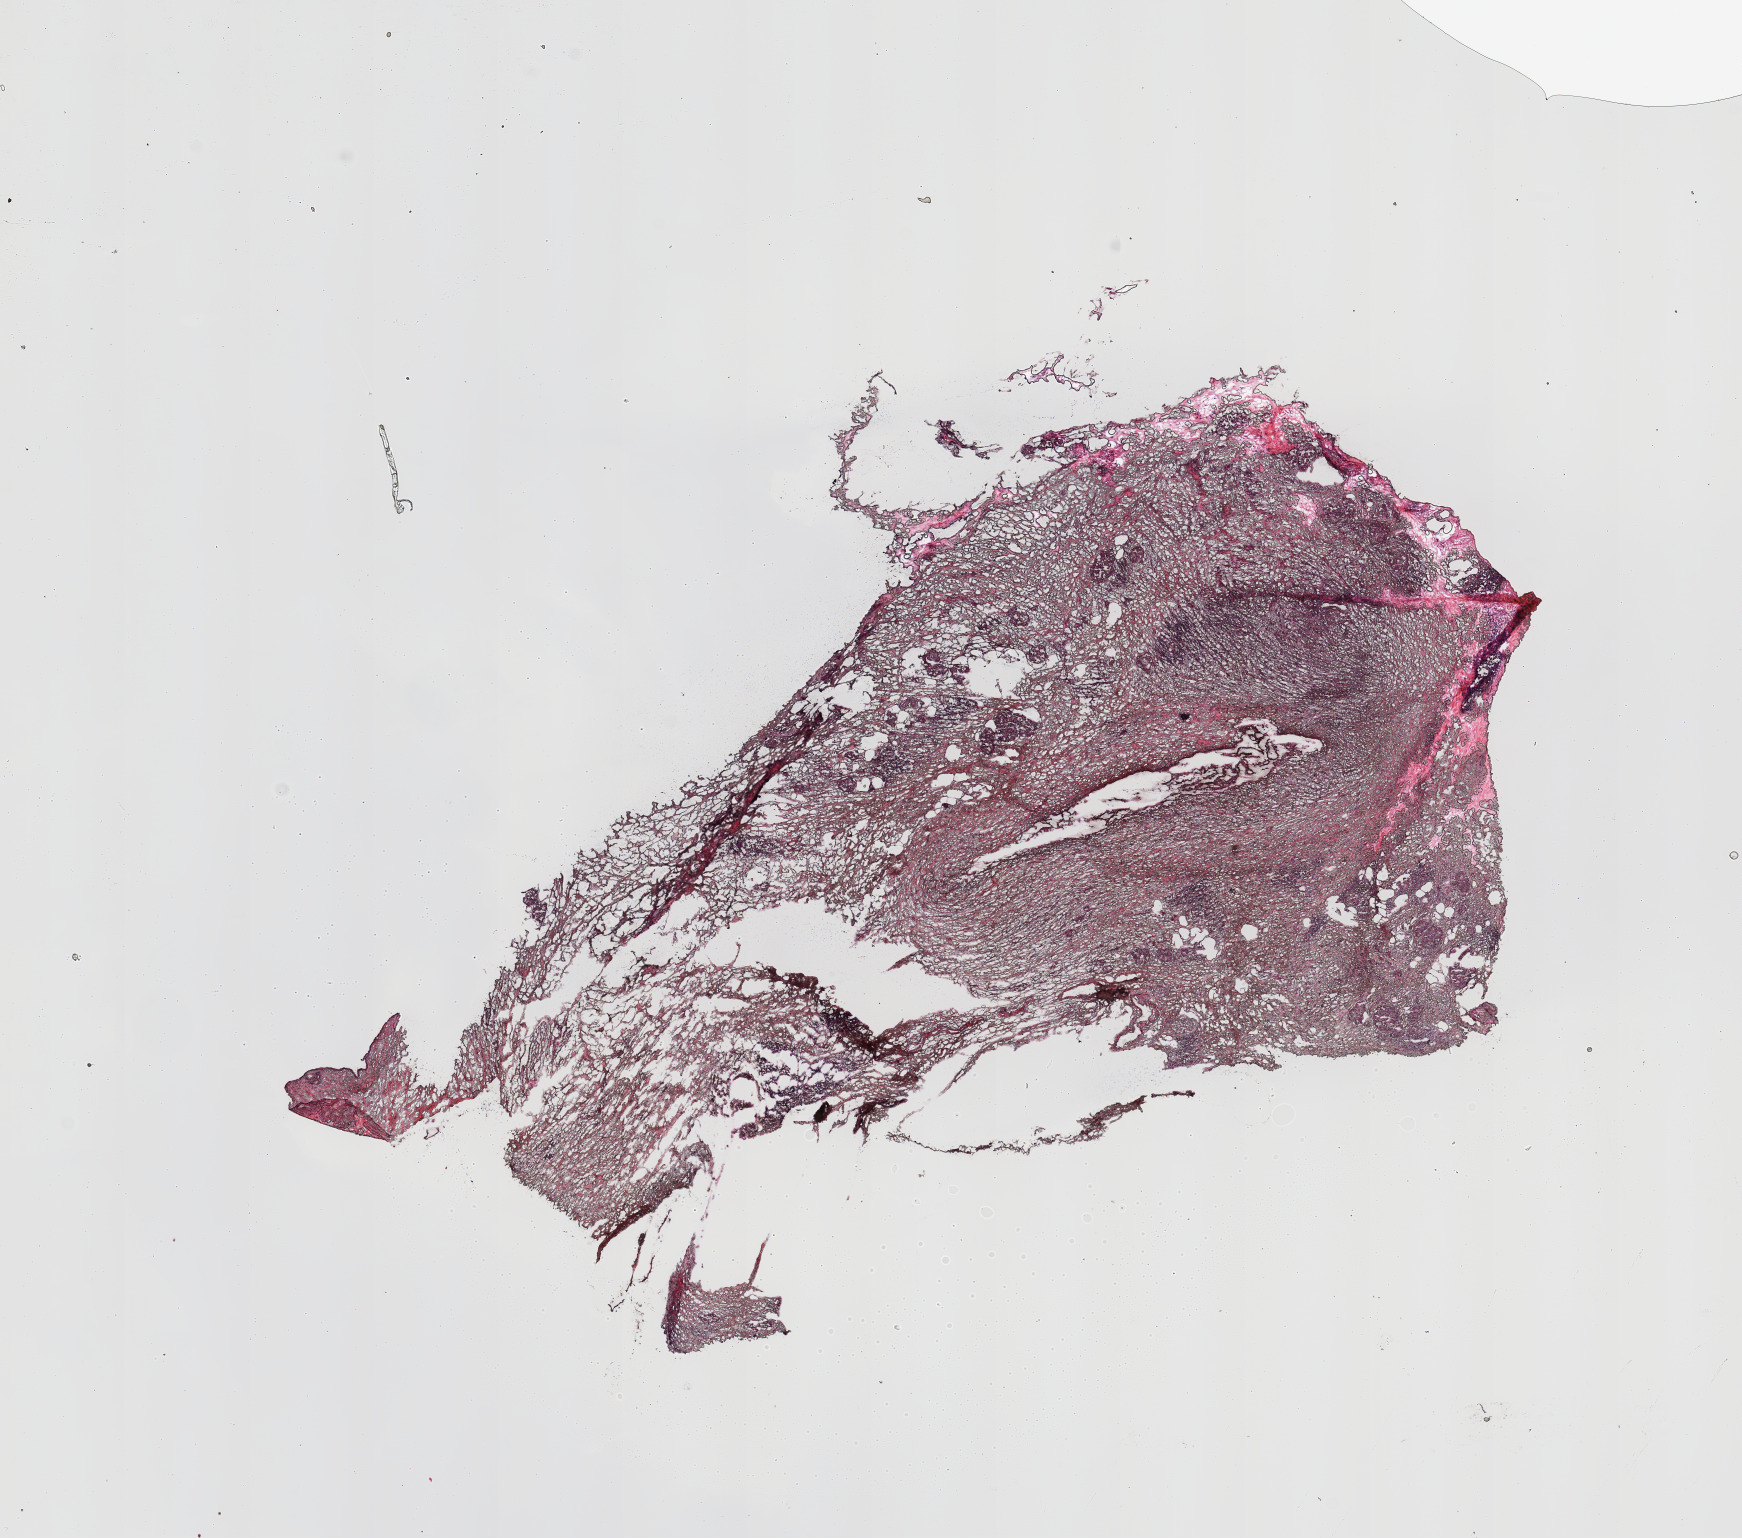
Hematoxylin and eosin (H&E) stained whole-slide image, low-resolution overview of the scanned area, about 13.8 x 12.2 mm (slide scanned at 20x); normal (non-tumour) tissue sample, sampled site: pancreas. Female, 59 y/o.
* this section: normal (non-tumour) tissue from the same patient
* patient diagnosis: Infiltrating duct carcinoma, NOS